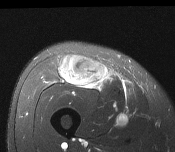
MRI of an extremity soft-tissue mass, one axial slice; position 66 of 116 along the scan axis; T2-weighted fat-saturated; MR volume resampled by the dataset authors to the PET/CT grid (not the native acquisition matrix); 175 × 152 image matrix. Male patient. From the clinical record (not read from this slice): histological type: pleiomorphic leiomyosarcoma; grade: intermediate; site of the primary tumour: right thigh.
Structures marked on this image (expert contour drawn on MRI and transferred to this co-registered scan by the dataset authors):
- gross tumour volume including surrounding oedema: box from (x=60, y=56) to (x=107, y=87) px